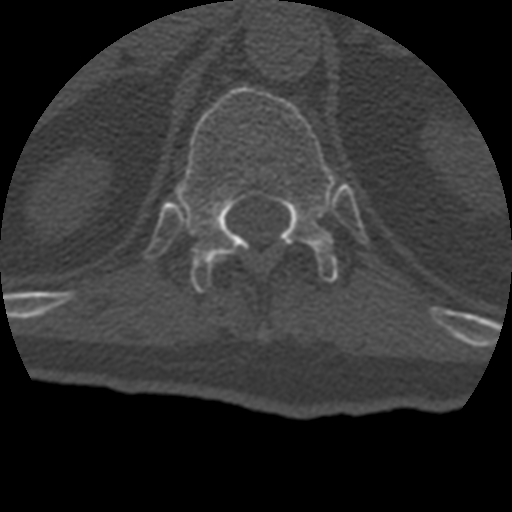
CT including the spine, one axial slice. Slice 181 of 399 in the series (ordered by position). 120 kVp. Bone window (W 1800 / L 400 HU). 1.25 mm slice thickness. 512 × 512 image matrix. Patient age 69 years. From the clinical record (not read from this slice): primary cancer: prostate.
Outlined on this slice (semi-automatically segmented with operator editing):
- T12 vertebra: bounding box [x1, y1, x2, y2] px = [175, 86, 339, 291]